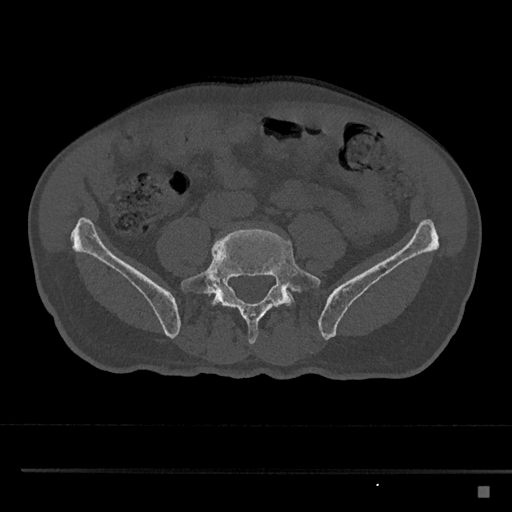
CT including the spine, one axial slice; position 584 of 797 along the scan axis; reconstruction kernel Br40s/3; bone window (W 1800 / L 400 HU); 512 × 512 image matrix, field of view 391 × 391 mm. Patient: male, 59 years. From the clinical record (not read from this slice): primary cancer: prostate.
Outlined on this slice (semi-automatically segmented with operator editing):
- L5 vertebra: bounding box <181,228,321,345> (left, top, right, bottom; pixels)